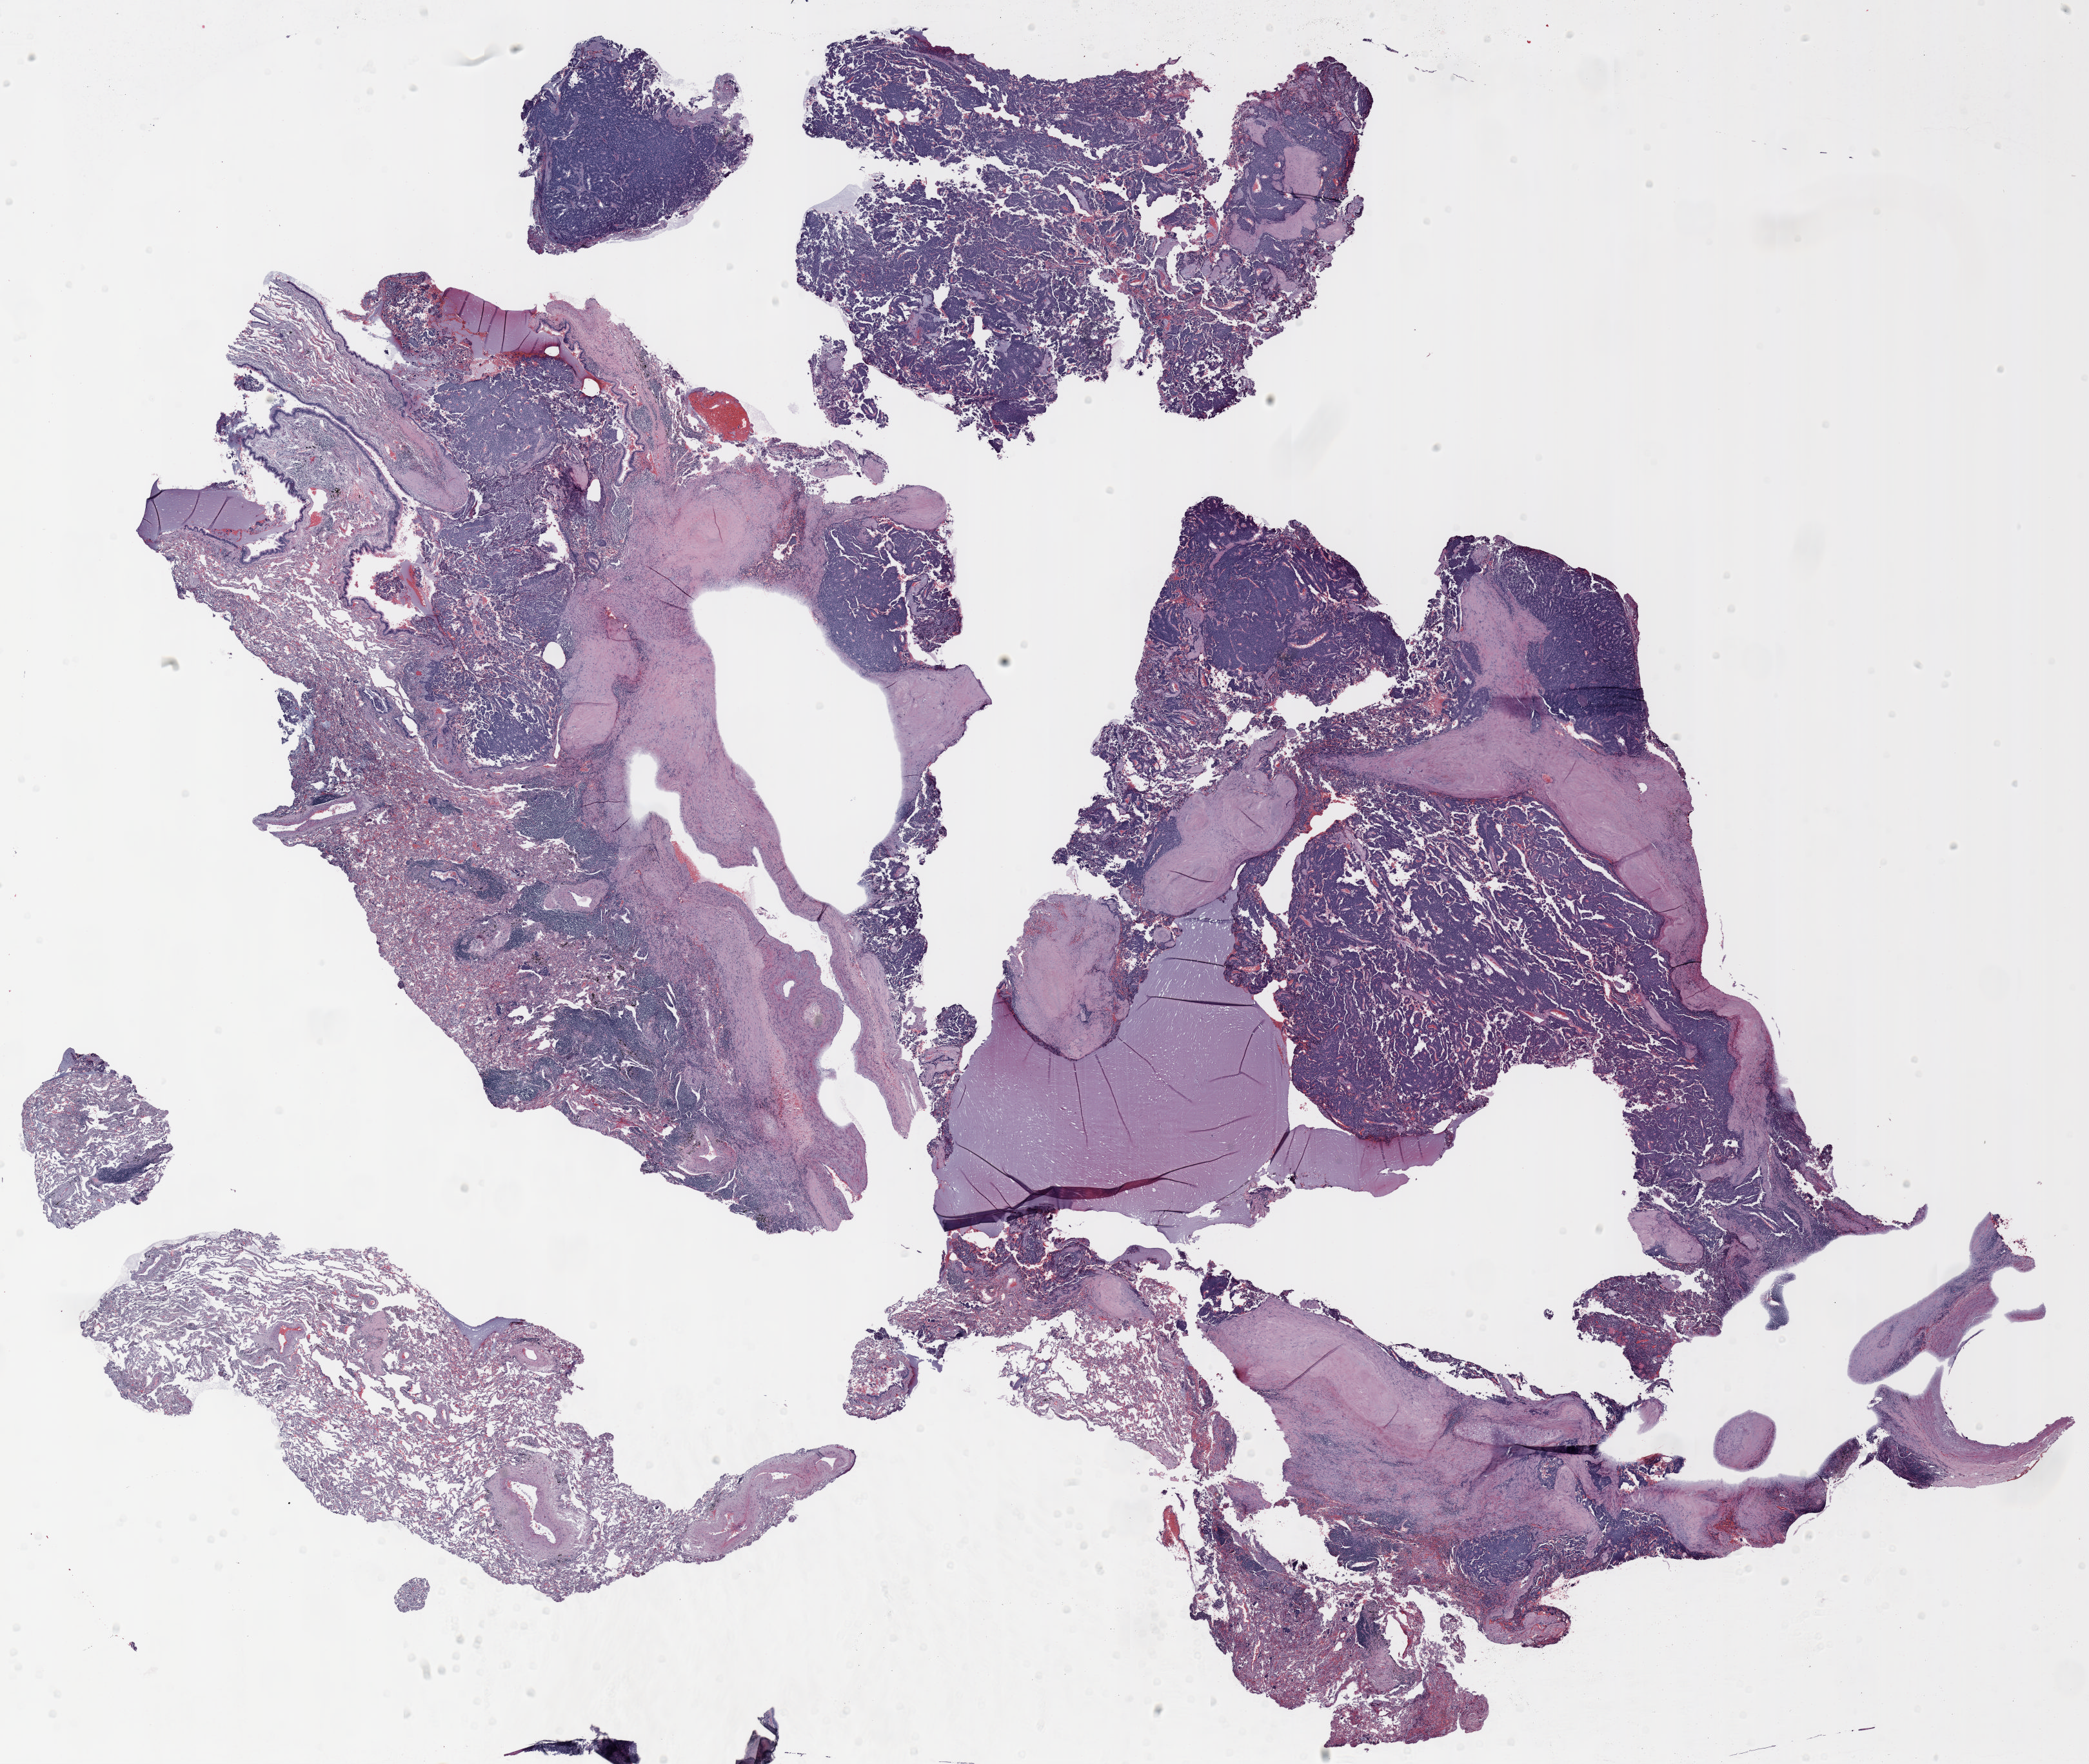
Whole-slide histology image, H&E-stained — shown as a low-resolution overview of the whole scanned area (about 26.0 x 22.0 mm), formalin-fixed paraffin-embedded (FFPE) section, lung. Male patient, aged 73 at enrolment. Grade: cannot be assessed (GX).
Stage (AJCC 6th edition): carcinoid, stage not assessed. ICD-O-3 topography: lower lobe of lung (C34.3). Participant's lung-cancer diagnosis: Carcinoid tumor, NOS (ICD-O-3 8240/3). Primary tumour location (clinical record): right lower lobe. Tumour size (pathology): 12 mm.